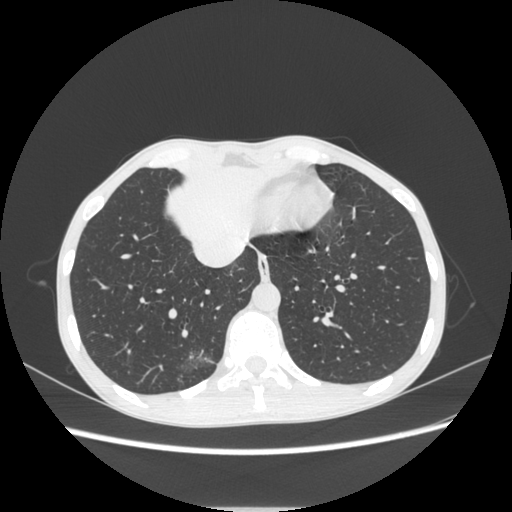
Chest CT, one axial slice; position 79 of 272 along the scan axis; reconstruction kernel STANDARD; lung window (W 1500 / L -600 HU); 512 × 512 image matrix, field of view 350 × 350 mm. Female patient, age 51 years. Case-level facts recorded for this patient, not image findings: clinical TNM (as recorded): T1c N0 M0; histopathological grade: G2-3.
Outlined on this slice (rectangle marked by the reading radiologist):
- lung tumour (recorded histology: adenocarcinoma): bounding box (x1, y1, x2, y2) in pixels: (173, 346, 219, 389)